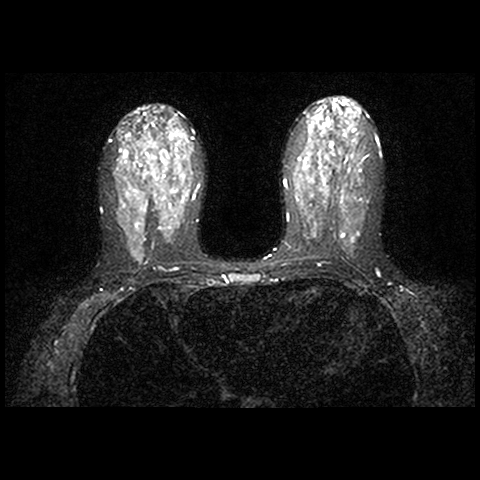
MRI of the breasts; 2 images, each one mid-volume slice chosen by position.
Image 1: axial T2-weighted / STIR image, series "STIR SENSE", slice 44 of 86, 2 mm slice thickness.
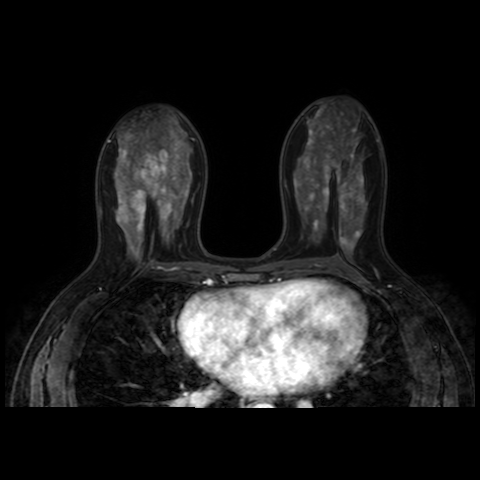
Image 2: post-contrast dynamic axial slice, slice 44 of 86, dynamic phase 5 of 8.
MRI impression (as recorded): RIGHT BREAST: There is moderate background enhancement. There is a well circumscribed, macro-lobulated T2 hyperintense lesion in the lateral right breast with T2 hypointense septations. This is best seen on series 301 image 41, located at 10:00. Overall it measures 1.9 x 1.7 x 1.7 cm with a total volume of 2.7 cc and demonstrates predominately progressive enhancement with a few scattered areas of plateau type enhancement. This is consistent with a fibroadenoma. There are other smaller lesions scattered throughout both breasts, similar in both in morphology and enhancement characteristics. They are more numerous on the right than on the left and measure up to 1.0 cm in size. These are most likely multiple fibroadenomata. Right breast is otherwise notable for multiple small circumscribed T2-hyperintense nonenhancing lesions consistent with simple cysts. No foci of suspicious enhancement, masses, or areas of architectural distortion seen within the right breast. Specifically, there is no MRI correlate for the suspicious hypoechoic lesion seen on prior ultrasound. There is no skin thickening, nipple inversion, or right axillary lymphadenopathy present. LEFT BREAST: There is moderate background enhancement. As detailed above, there are multiple well-defined T2 hyperintense lesions with predominantly progressive enhancement most consistent with fibroadenomata. Additionally, small T2 hyperintense nonenhancing lesions are seen consistent with simple cysts, the largest measuring up to 7 mm in the central left breast. No foci of suspicious enhancement, masses, or areas of architectural distortion seen within the left breast. There is no skin thickening, nipple inversion, or left axillary lymphadenopathy present.
Patient-level pathology facts (from the clinical record, not from the images): pathology diagnosis: benign fibroadenoma (right breast); pathology report notes: RIGHT BREAST CALCIFICATION WITH NEEDLE LOCATION: FIBROADENOMA (1.9CM). REMAINING BREAST TISSUE WITH ADENOSIS, FOCAL FIBROADENOMATOUS CHANGES, APOCRINE METAPLASIA, FIBROCYSTIC CHANGES, SMALL INTRADUCTAL PAPILLOMAS, AND USUAL TYPE DUCTAL HYPERPLASIA. MICROCALCIFICATIONS ASSOCIATED WITH BENIGN BREAST TISSUE ARE IDENTIFIED. NO IN-SITU OR INVASIVE CARCINOMA.